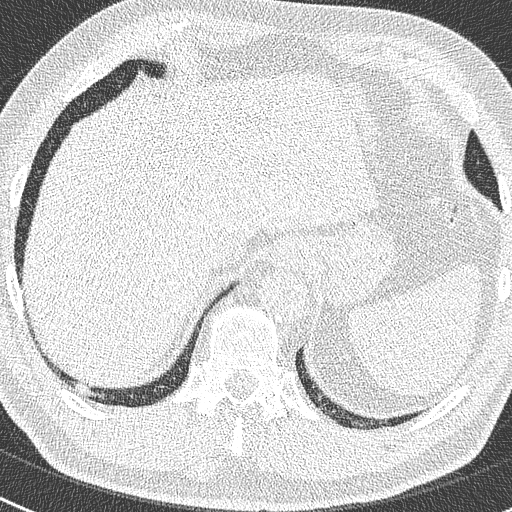
Low-dose screening chest CT, axial slice, second screening round (one year after baseline), lung window (W 1500 / L -600 HU), 2 mm slice thickness, 512 × 512 image matrix. Male participant, aged 63 years at enrolment.
- Expert-annotated lung lesion, bounding box <66,377,99,404> (left, top, right, bottom; pixels).
- No non-calcified nodule or mass ≥4 mm was recorded by the screening reader at this exam.
- Lung cancer was diagnosed 262 days after this screen: adenocarcinoma, NOS, right lower lobe, moderately differentiated (G2), stage IIIB (AJCC 6th edition), 17 mm at pathology.